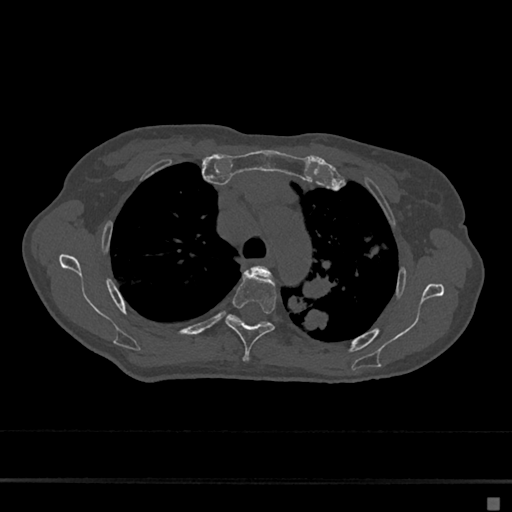
CT including the spine, one axial slice. Position 497 of 797 along the scan axis. Reconstruction kernel Br40s/3. Bone window (W 1800 / L 400 HU). 512 × 512 image matrix. Female patient, age 68 years. Case-level facts recorded for this patient, not image findings: primary cancer: renal.
Outlined on this slice (semi-automatic segmentation, software-assisted and operator-edited):
- T3 vertebra: bounding box <254,266,270,274> (left, top, right, bottom; pixels)
- T4 vertebra: <225,273,276,362>
- T5 vertebra: <228,315,267,326>